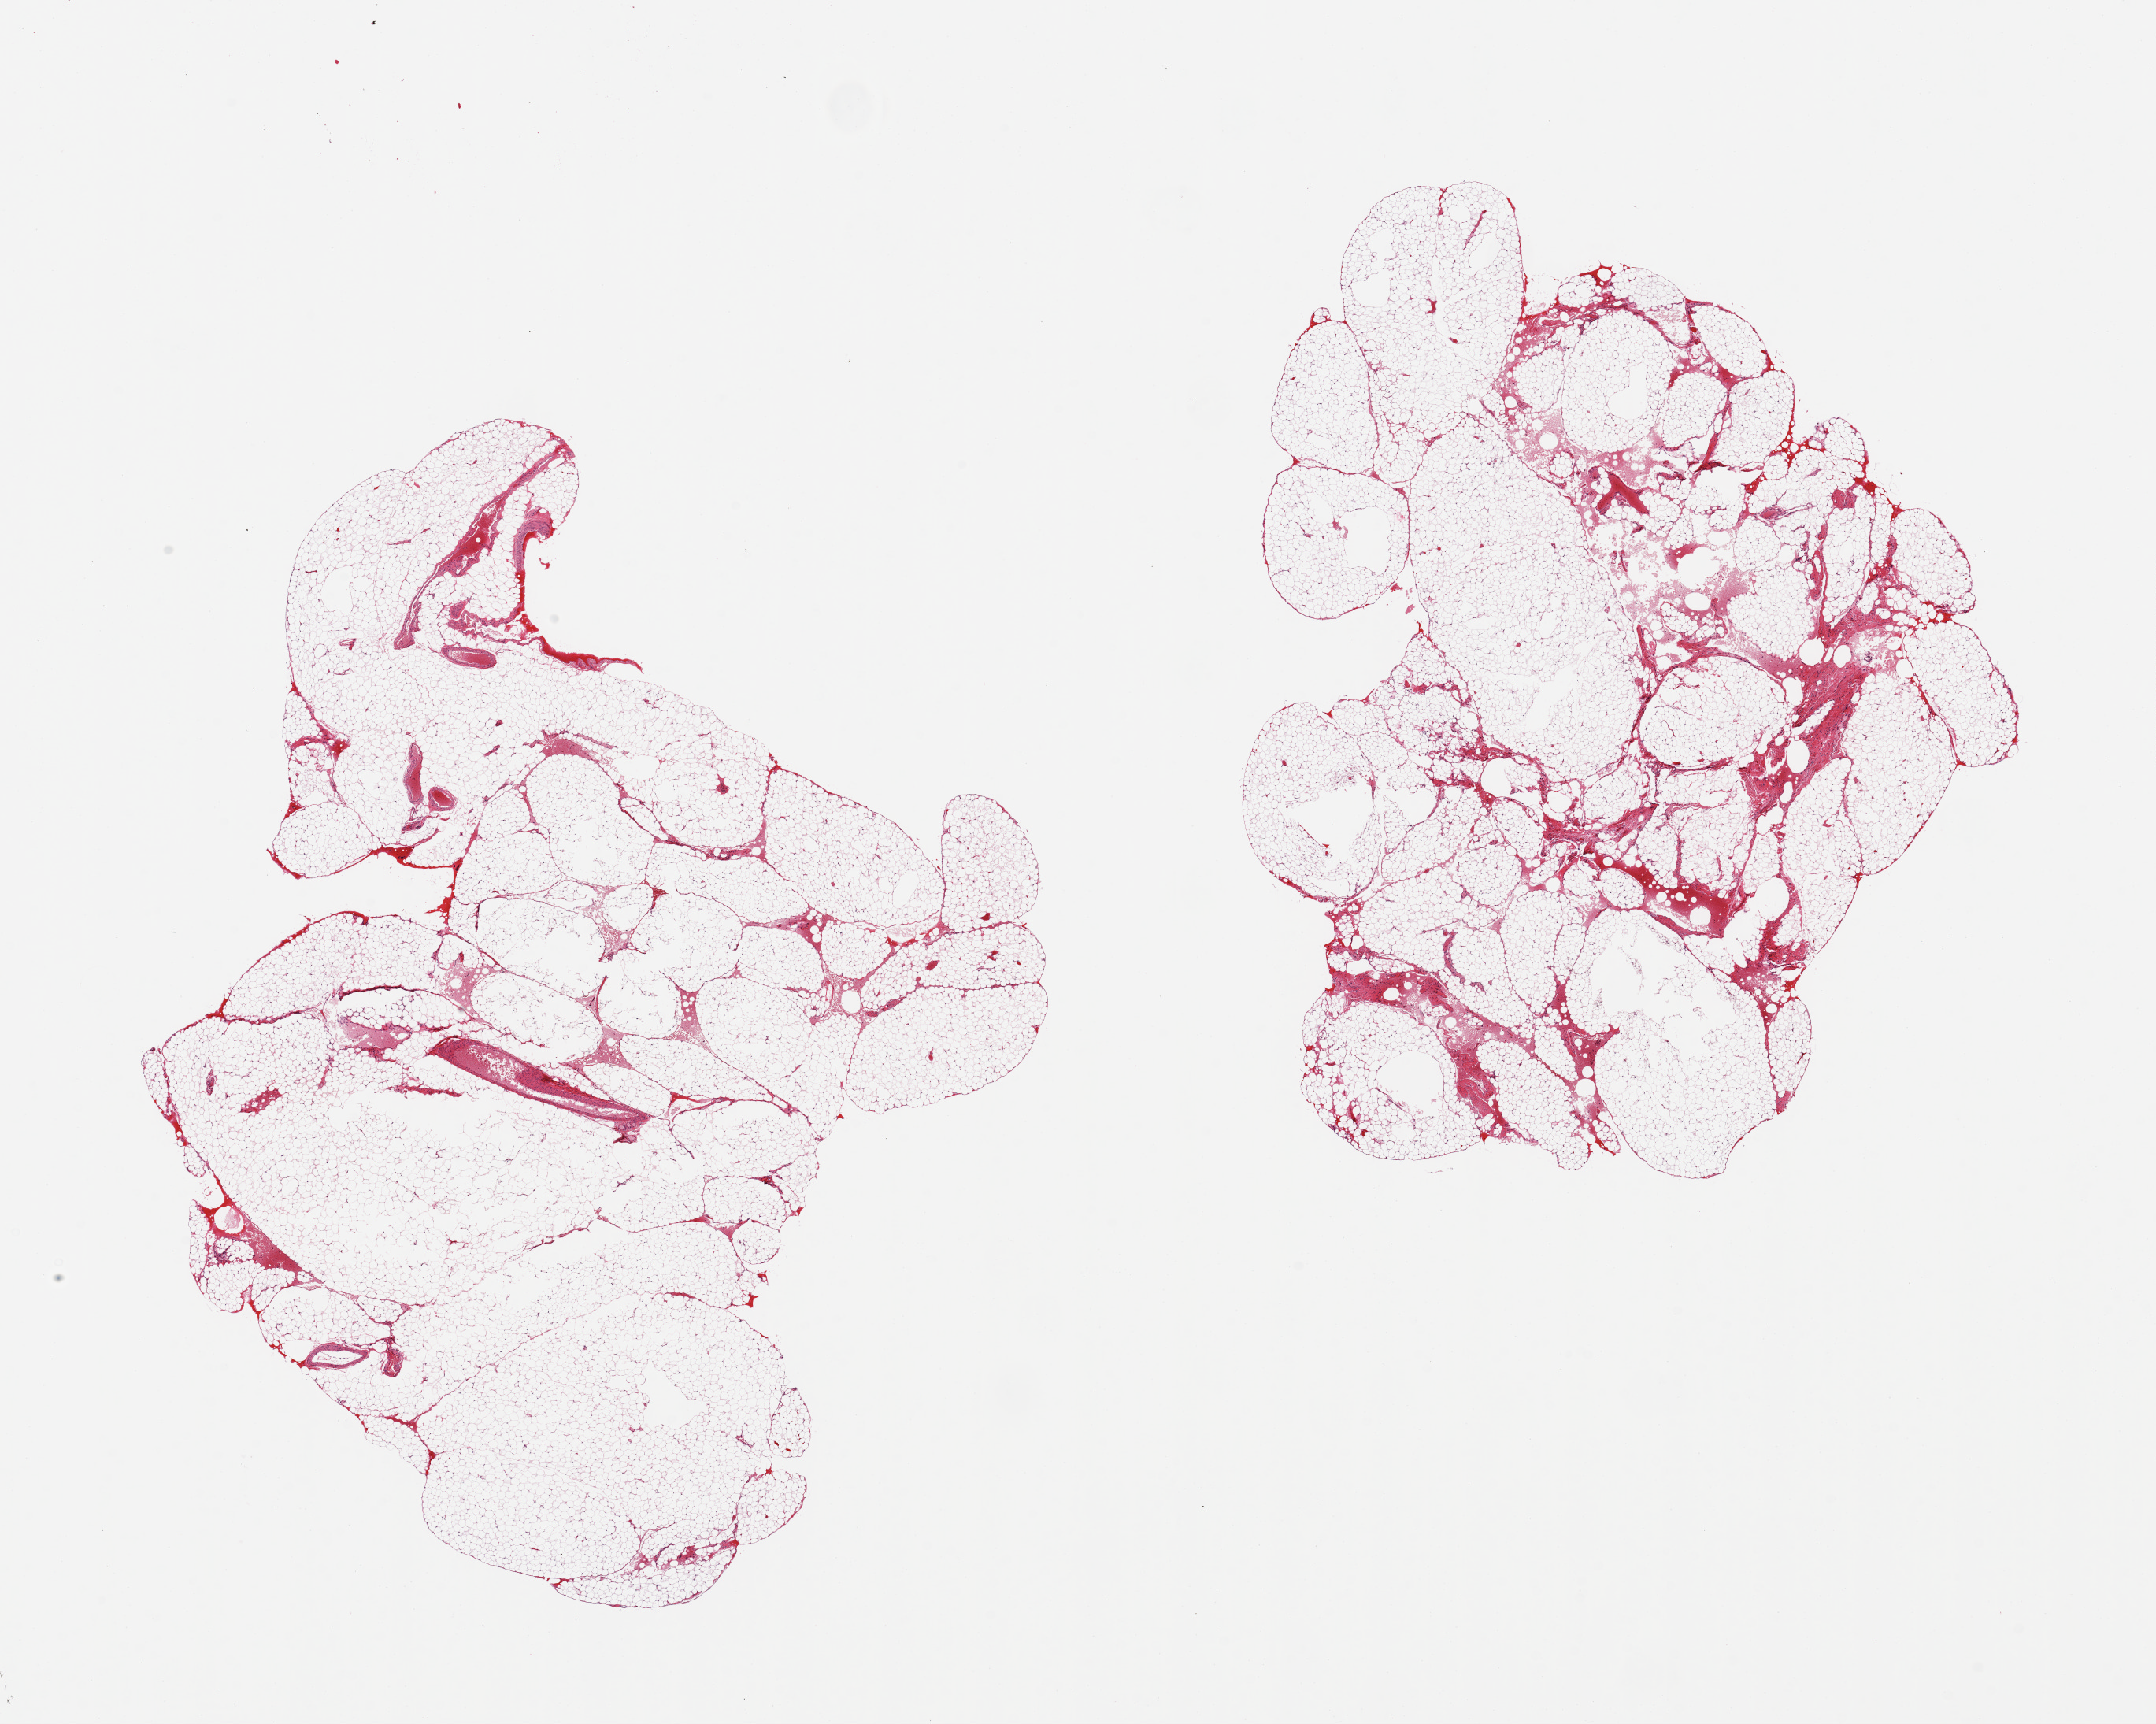
Hematoxylin and eosin (H&E) whole-slide image, brightfield, low-resolution overview of the scanned area, about 21.7 x 17.3 mm (slide scanned at 20x), PAXgene-fixed paraffin-embedded (PFPE) section, sampled site (target tissue): omentum, donor tissue sample. Donor sex: female.
Reviewer comment on this tissue sample: 2 pieces, fascia/vascular elements are ~15-20% tissue.